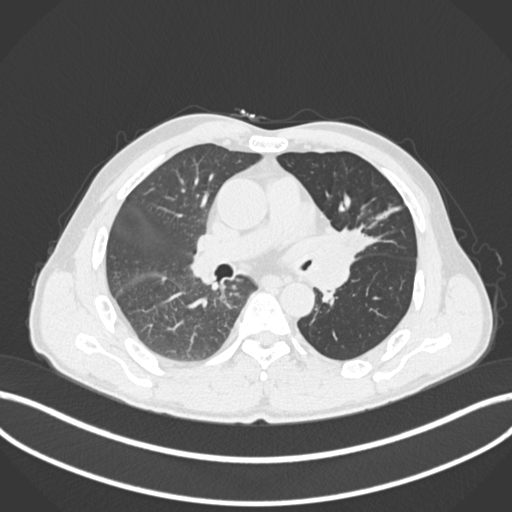
Chest CT, one axial slice; 120 kVp; lung window (W 1500 / L -600 HU); 512 × 512 image matrix. Patient: male, 57 years. Case-level facts recorded for this patient, not image findings: clinical TNM (as recorded): T2b N0 M0.
Annotated regions visible in this slice (rectangle marked by the reading radiologist):
- lung tumour (recorded histology: squamous cell carcinoma): box from (x=308, y=218) to (x=378, y=267) px